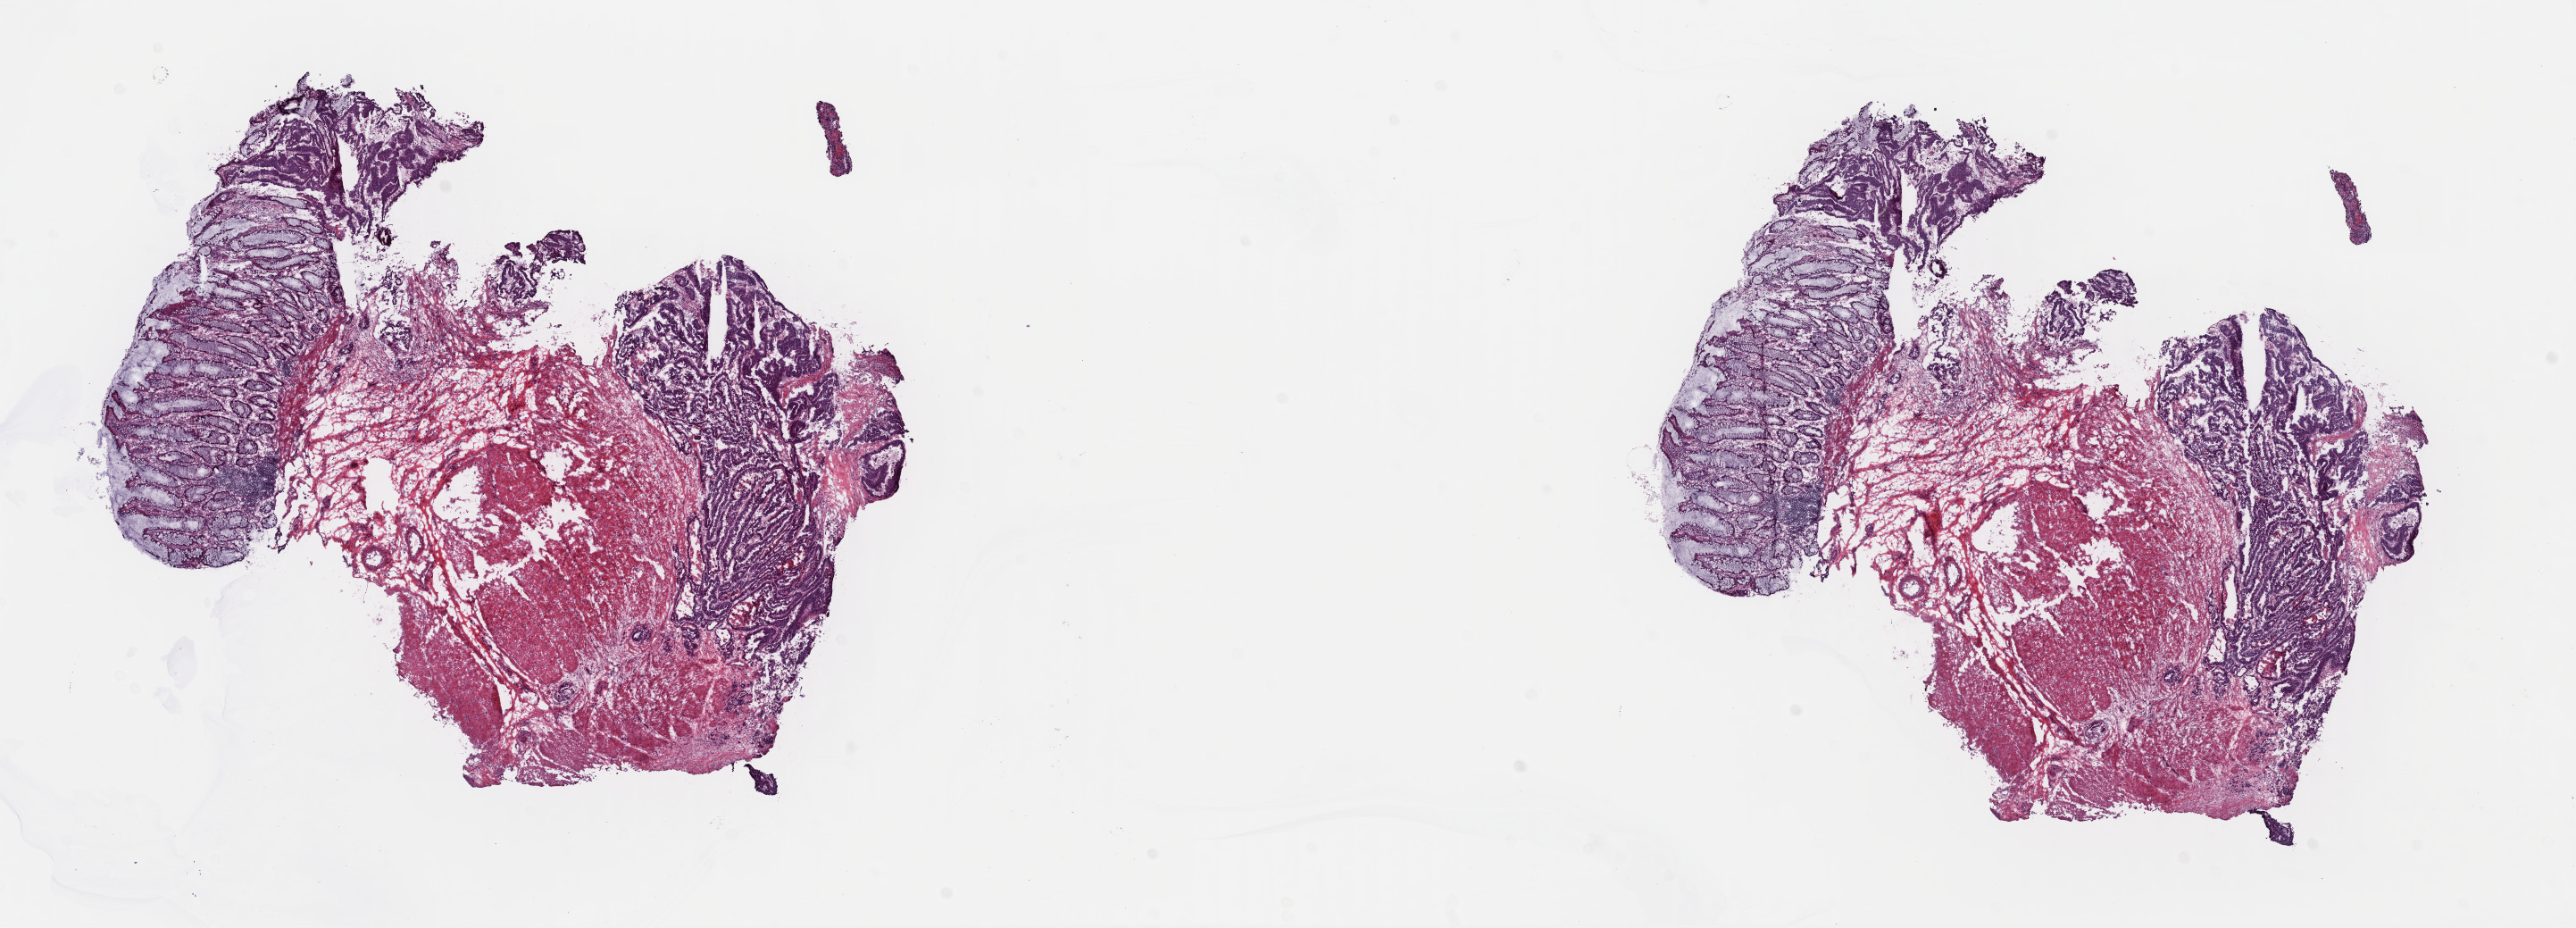
Whole-slide histology image, Hematoxylin and eosin (H&E) stained, a low-resolution overview of the entire scanned area, about 22.7 x 8.2 mm (slide scanned at 40x); frozen section from the top of the tissue portion; primary tumour sample from the colon. Male patient; age at initial diagnosis 56 years.
Pathologic diagnosis: Adenocarcinoma, NOS.